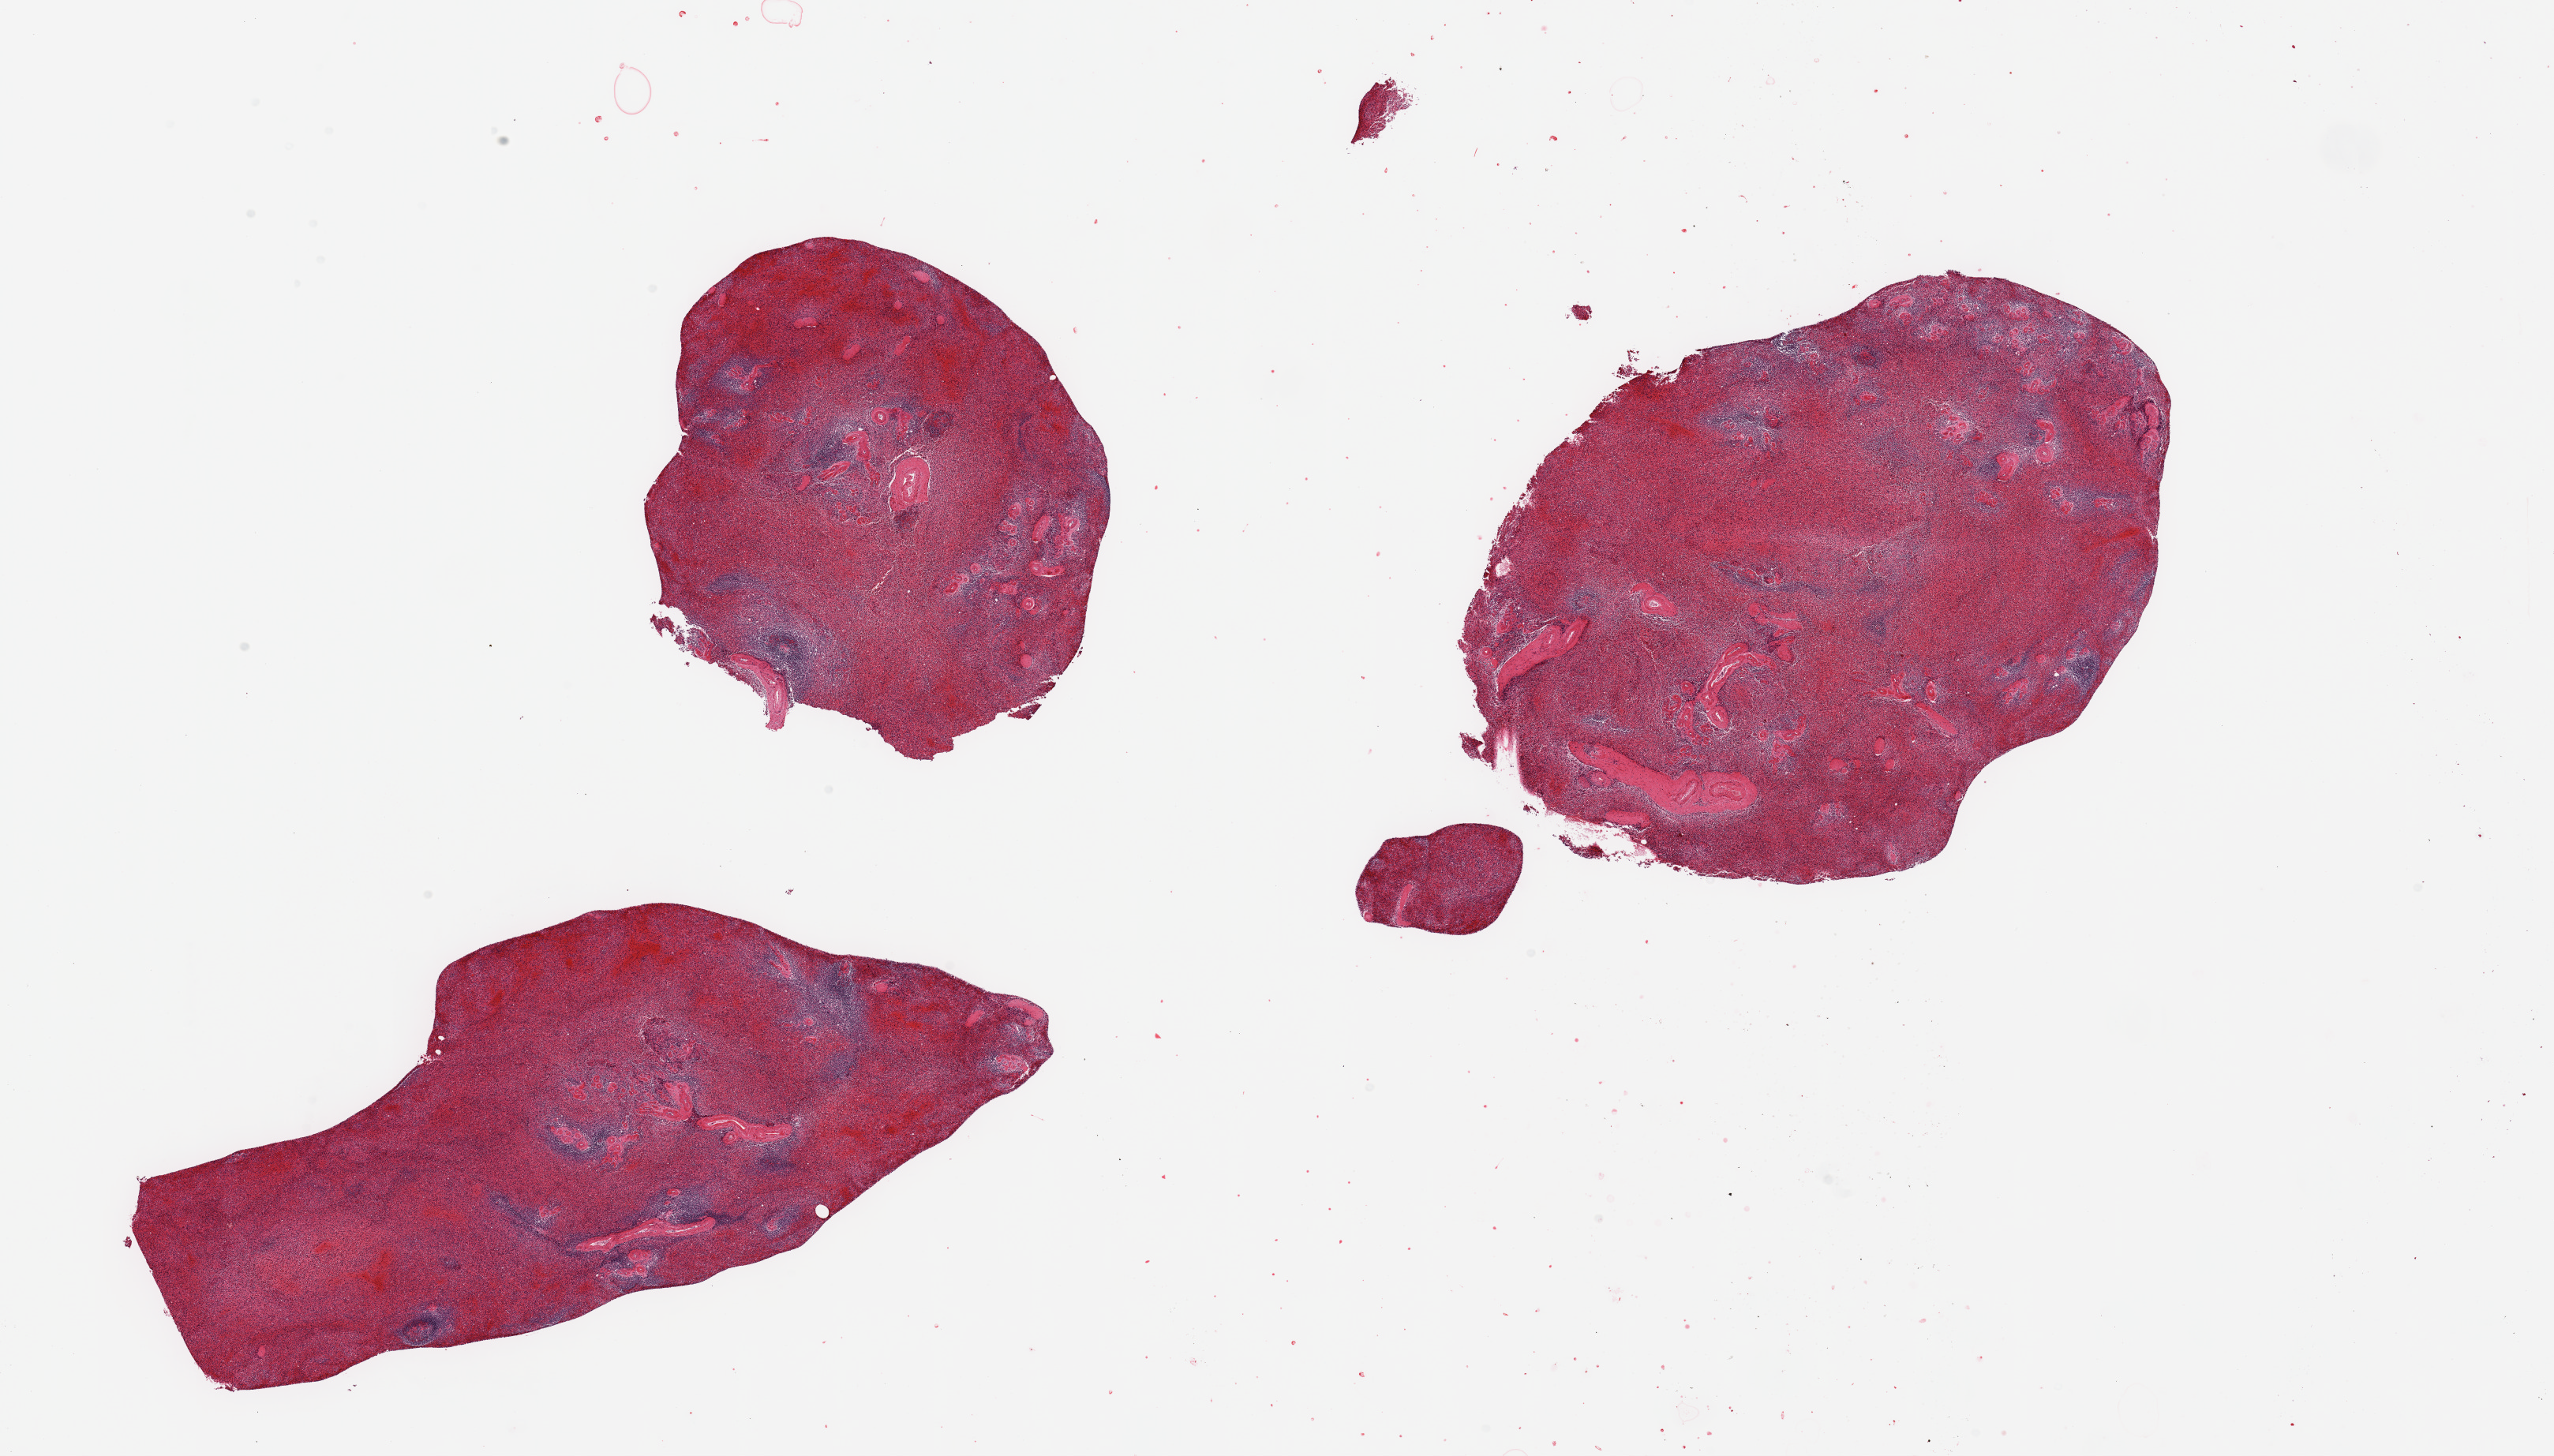
Digitized H&E-stained section, brightfield, low-resolution overview of the scanned area, about 25.6 x 14.6 mm (slide scanned at 20x); PAXgene-fixed, paraffin-embedded tissue; section of spleen (target tissue); donor tissue sample.
Pathologist's review note for this sample: 3 pieces; congested.